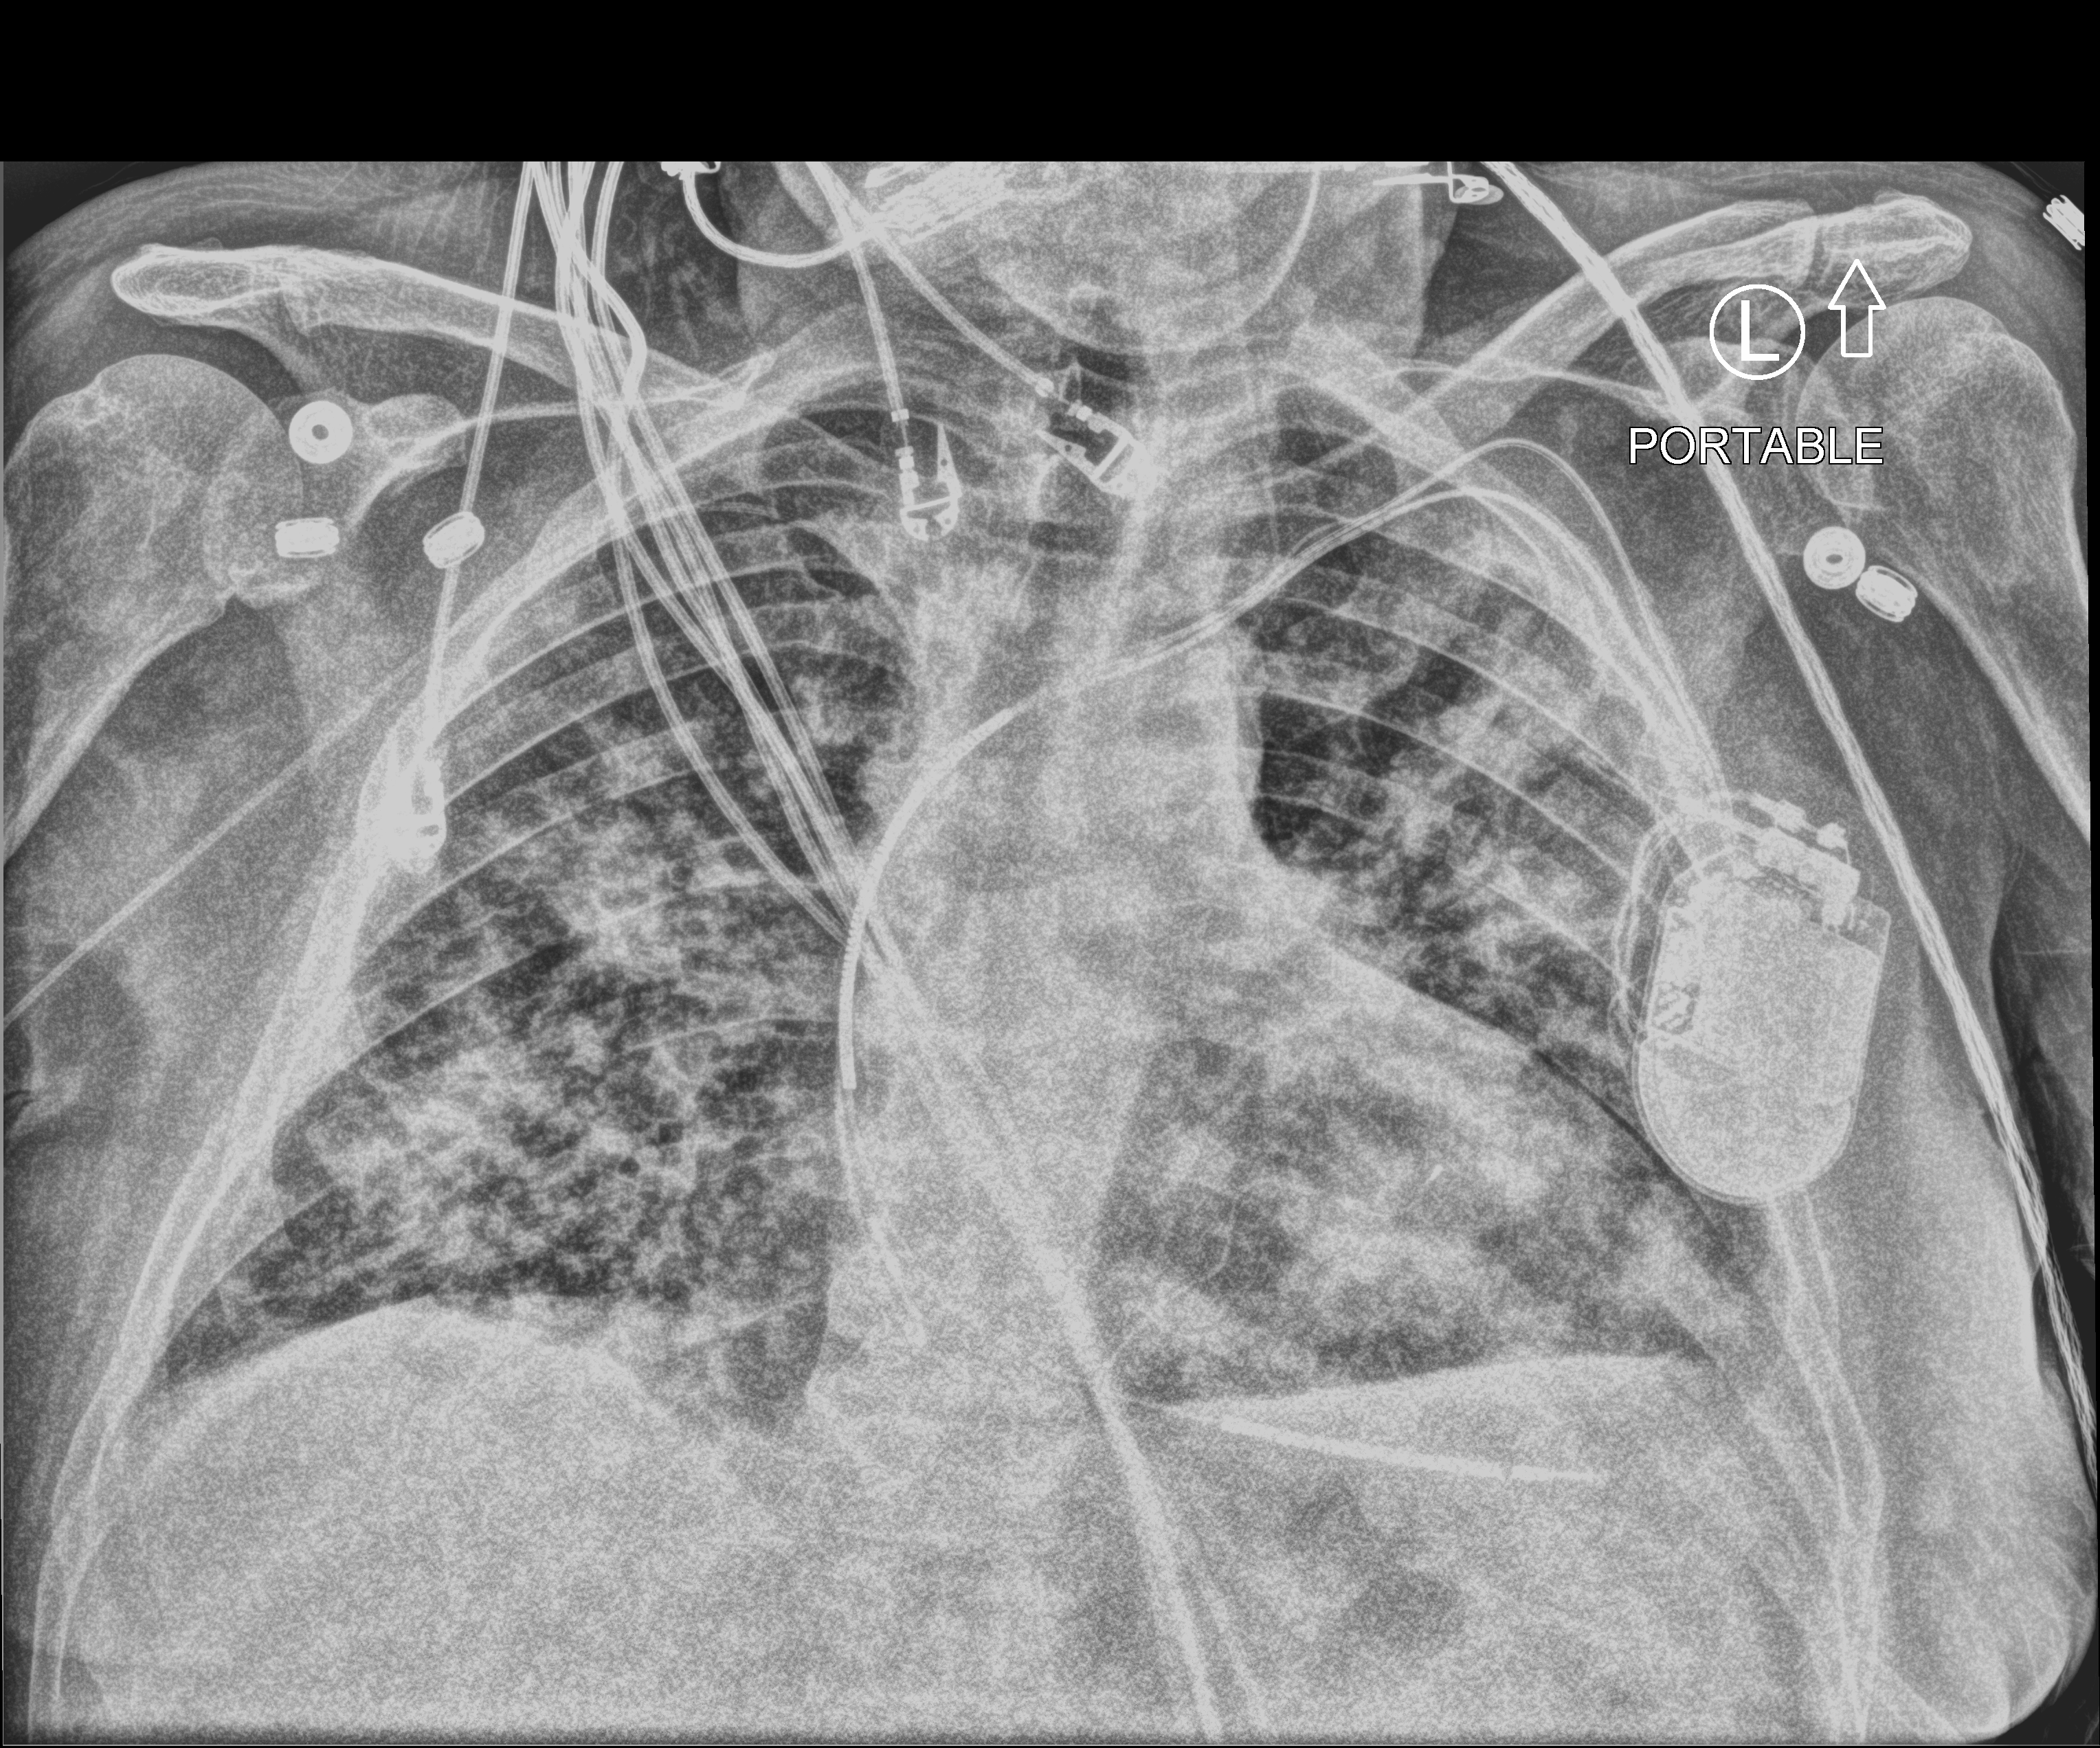
Bedside chest radiograph (computed radiography), anteroposterior (AP) projection. Male patient hospitalised with COVID-19, age 60–74 years.
Admission-level facts for this patient (not findings on this image; timing relative to this image not recorded): length of hospital stay: 27 days.